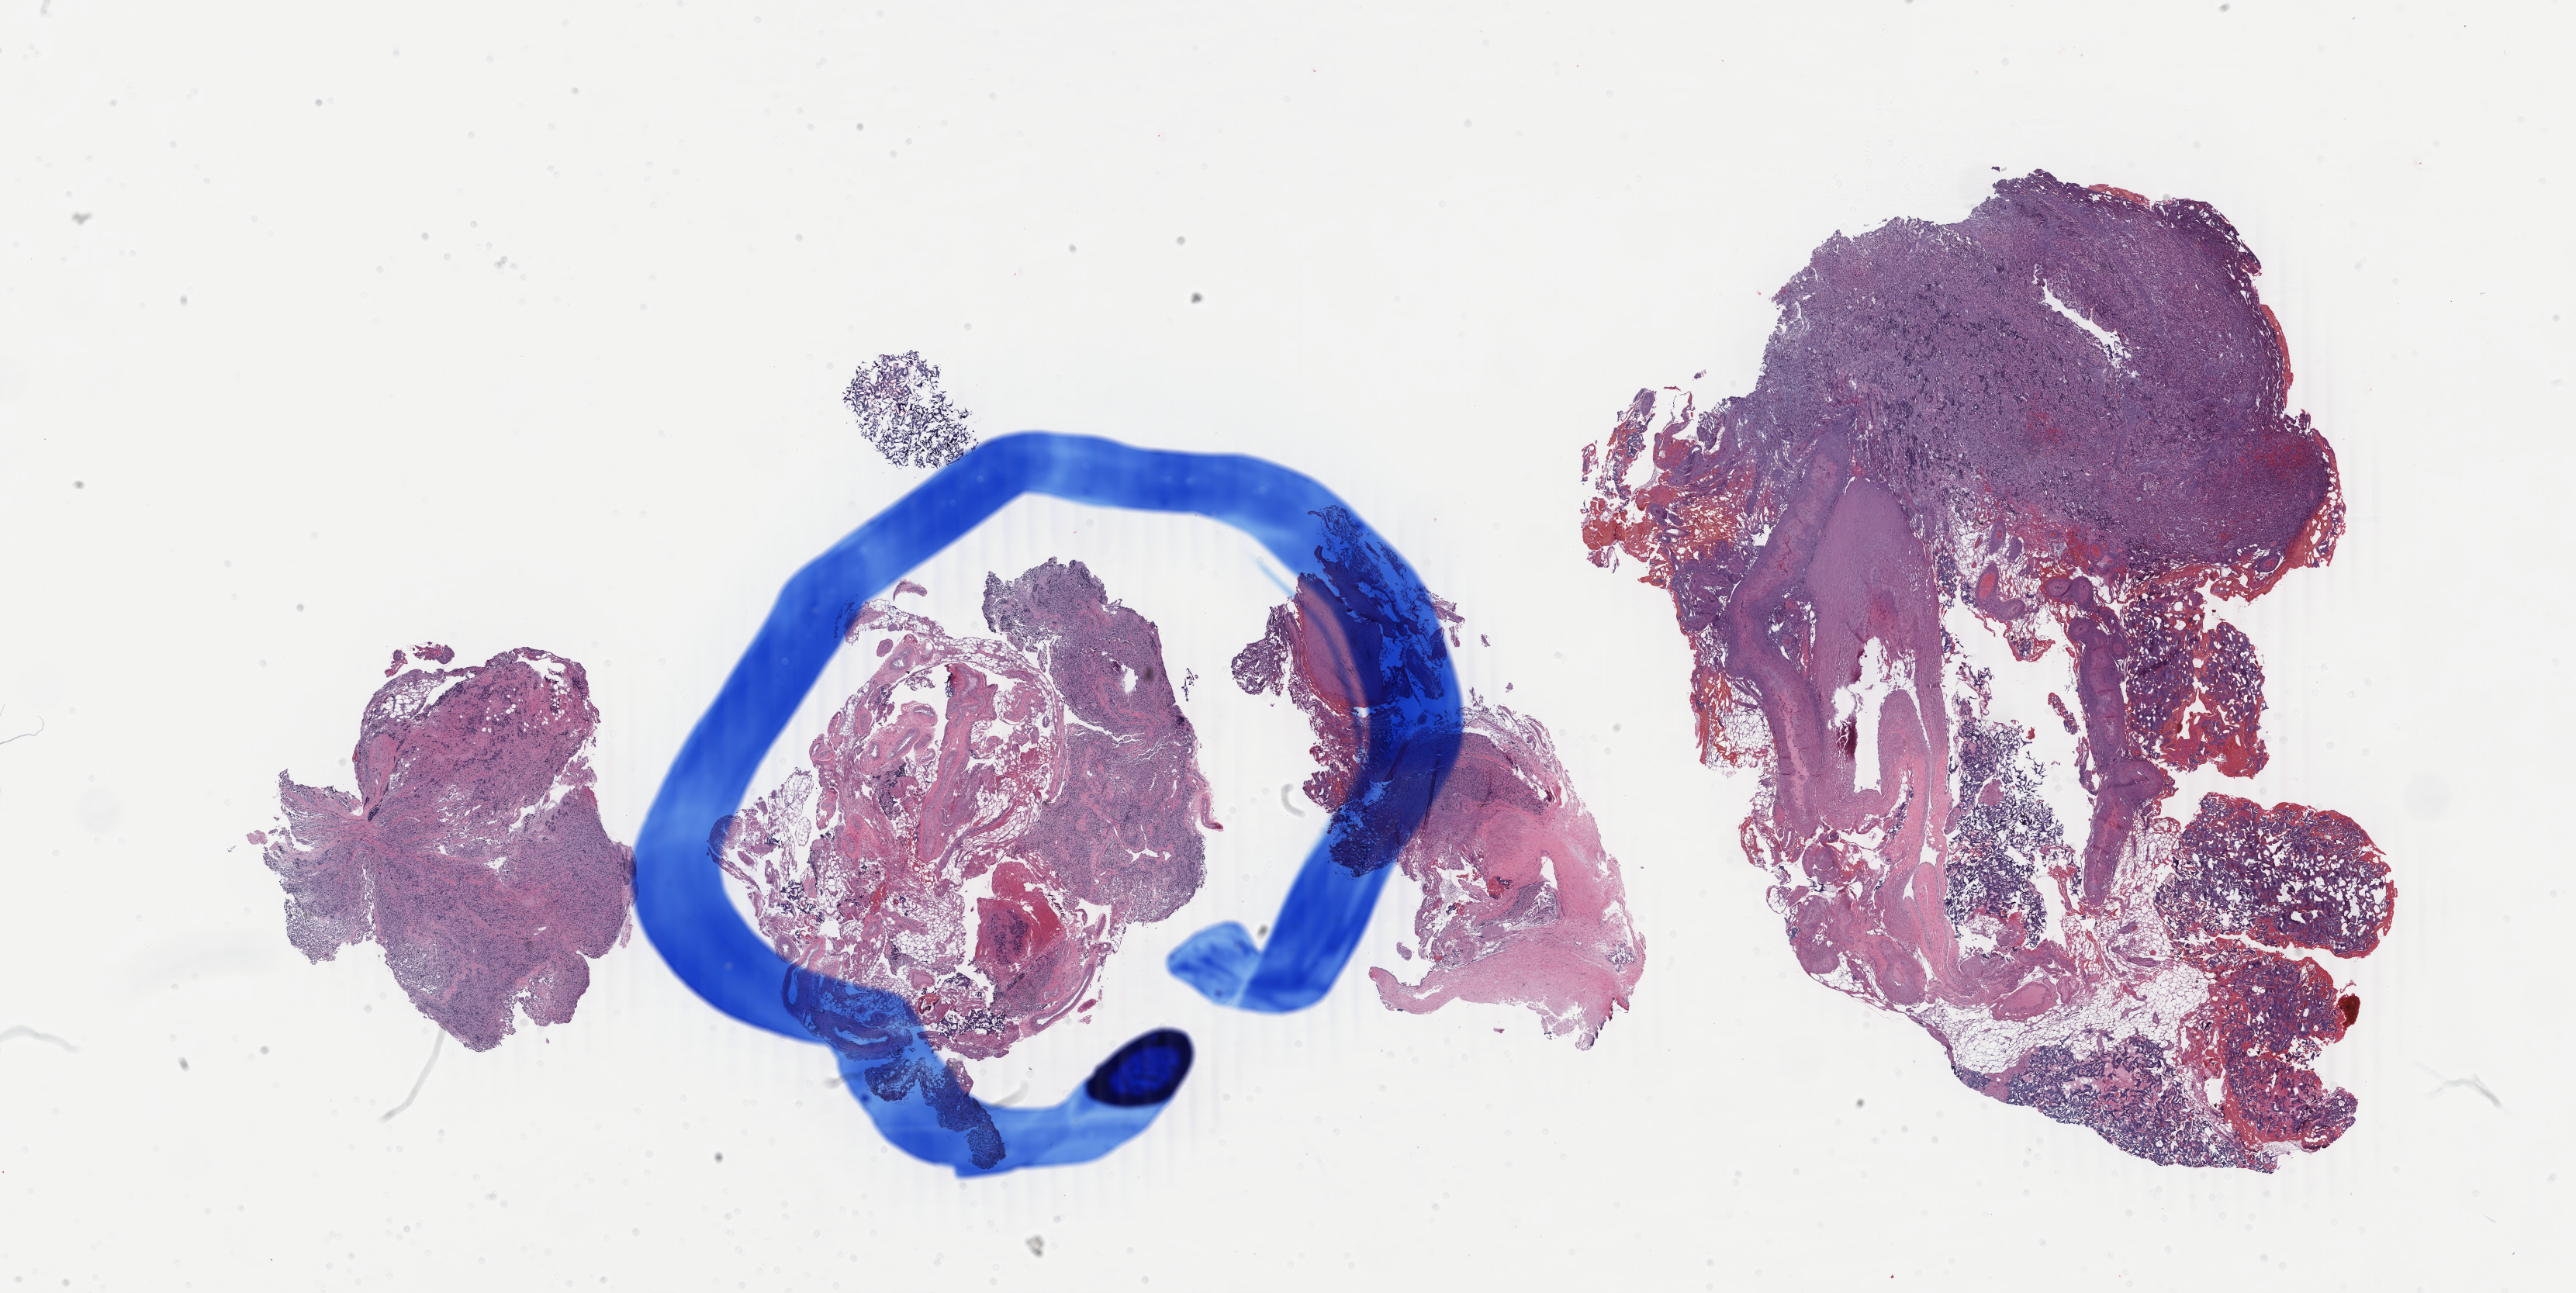
H&E whole-slide image, shown as a low-resolution overview of the whole scanned area (about 26.4 x 13.3 mm); FFPE section; spinal cord, cranial nerves, and other parts of central nervous system, primary tumour sample. Patient: male, age at initial diagnosis 55 years.
• pathologic diagnosis: Paraganglioma, malignant (nervous system, NOS)